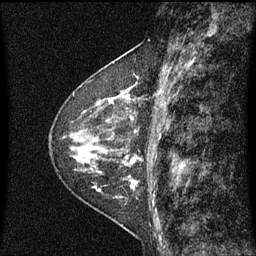
Breast MRI (dynamic contrast-enhanced), one sagittal slice; slice 26 of 60 in the series (ordered by position); dynamic contrast-enhanced series, image 2 of 3 at this slice position (ordered by acquisition); 1.5 T; TE 4.2 ms, TR 8 ms; 256 × 256 image matrix, field of view 200 × 200 mm. Patient: female, 48 years.
Structures marked on this image (semi-automatically segmented with operator editing):
- analysis volume of interest (the breast-tissue region the enhancement analysis was run in; not a lesion): bounding box [x1, y1, x2, y2] px = [103, 74, 145, 139]
- tumour enhancement mask (voxels above the 70 % enhancement threshold inside the analysis volume of interest): [108, 76, 139, 119]